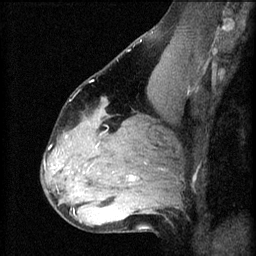
Breast MRI (dynamic contrast-enhanced), one sagittal slice; position 38 of 60 along the scan axis; 3 images stored at this slice position (order not interpretable as contrast timing); 1.5 T; TE 4.2 ms, TR 8.2 ms; 256 × 256 image matrix, field of view 180 × 180 mm. Patient: female, 37 years.
Outlined on this slice (semi-automatically segmented with operator editing):
- analysis volume of interest (the breast-tissue region the enhancement analysis was run in; not a lesion): bounding box (x1, y1, x2, y2) in pixels: (67, 120, 122, 179)
- tumour enhancement mask (voxels above the 70 % enhancement threshold inside the analysis volume of interest): (96, 146, 98, 149)